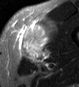
MRI of an extremity soft-tissue mass, one axial slice. Slice 29 of 45 in the series (ordered by position). STIR. MR volume resampled by the dataset authors to the PET/CT grid (not the native acquisition matrix). 3.27 mm slice thickness. 79 × 87 image matrix, field of view 77 × 85 mm. Male patient. From the clinical record (not read from this slice): histological type: pleiomorphic leiomyosarcoma; grade: high; site of the primary tumour: left thigh.
Structures marked on this image (expert contour drawn on MRI and transferred to this co-registered scan by the dataset authors):
- gross tumour volume including surrounding oedema: bounding box [x1, y1, x2, y2] px = [18, 18, 57, 60]
- gross tumour volume (mass): [22, 25, 48, 58]